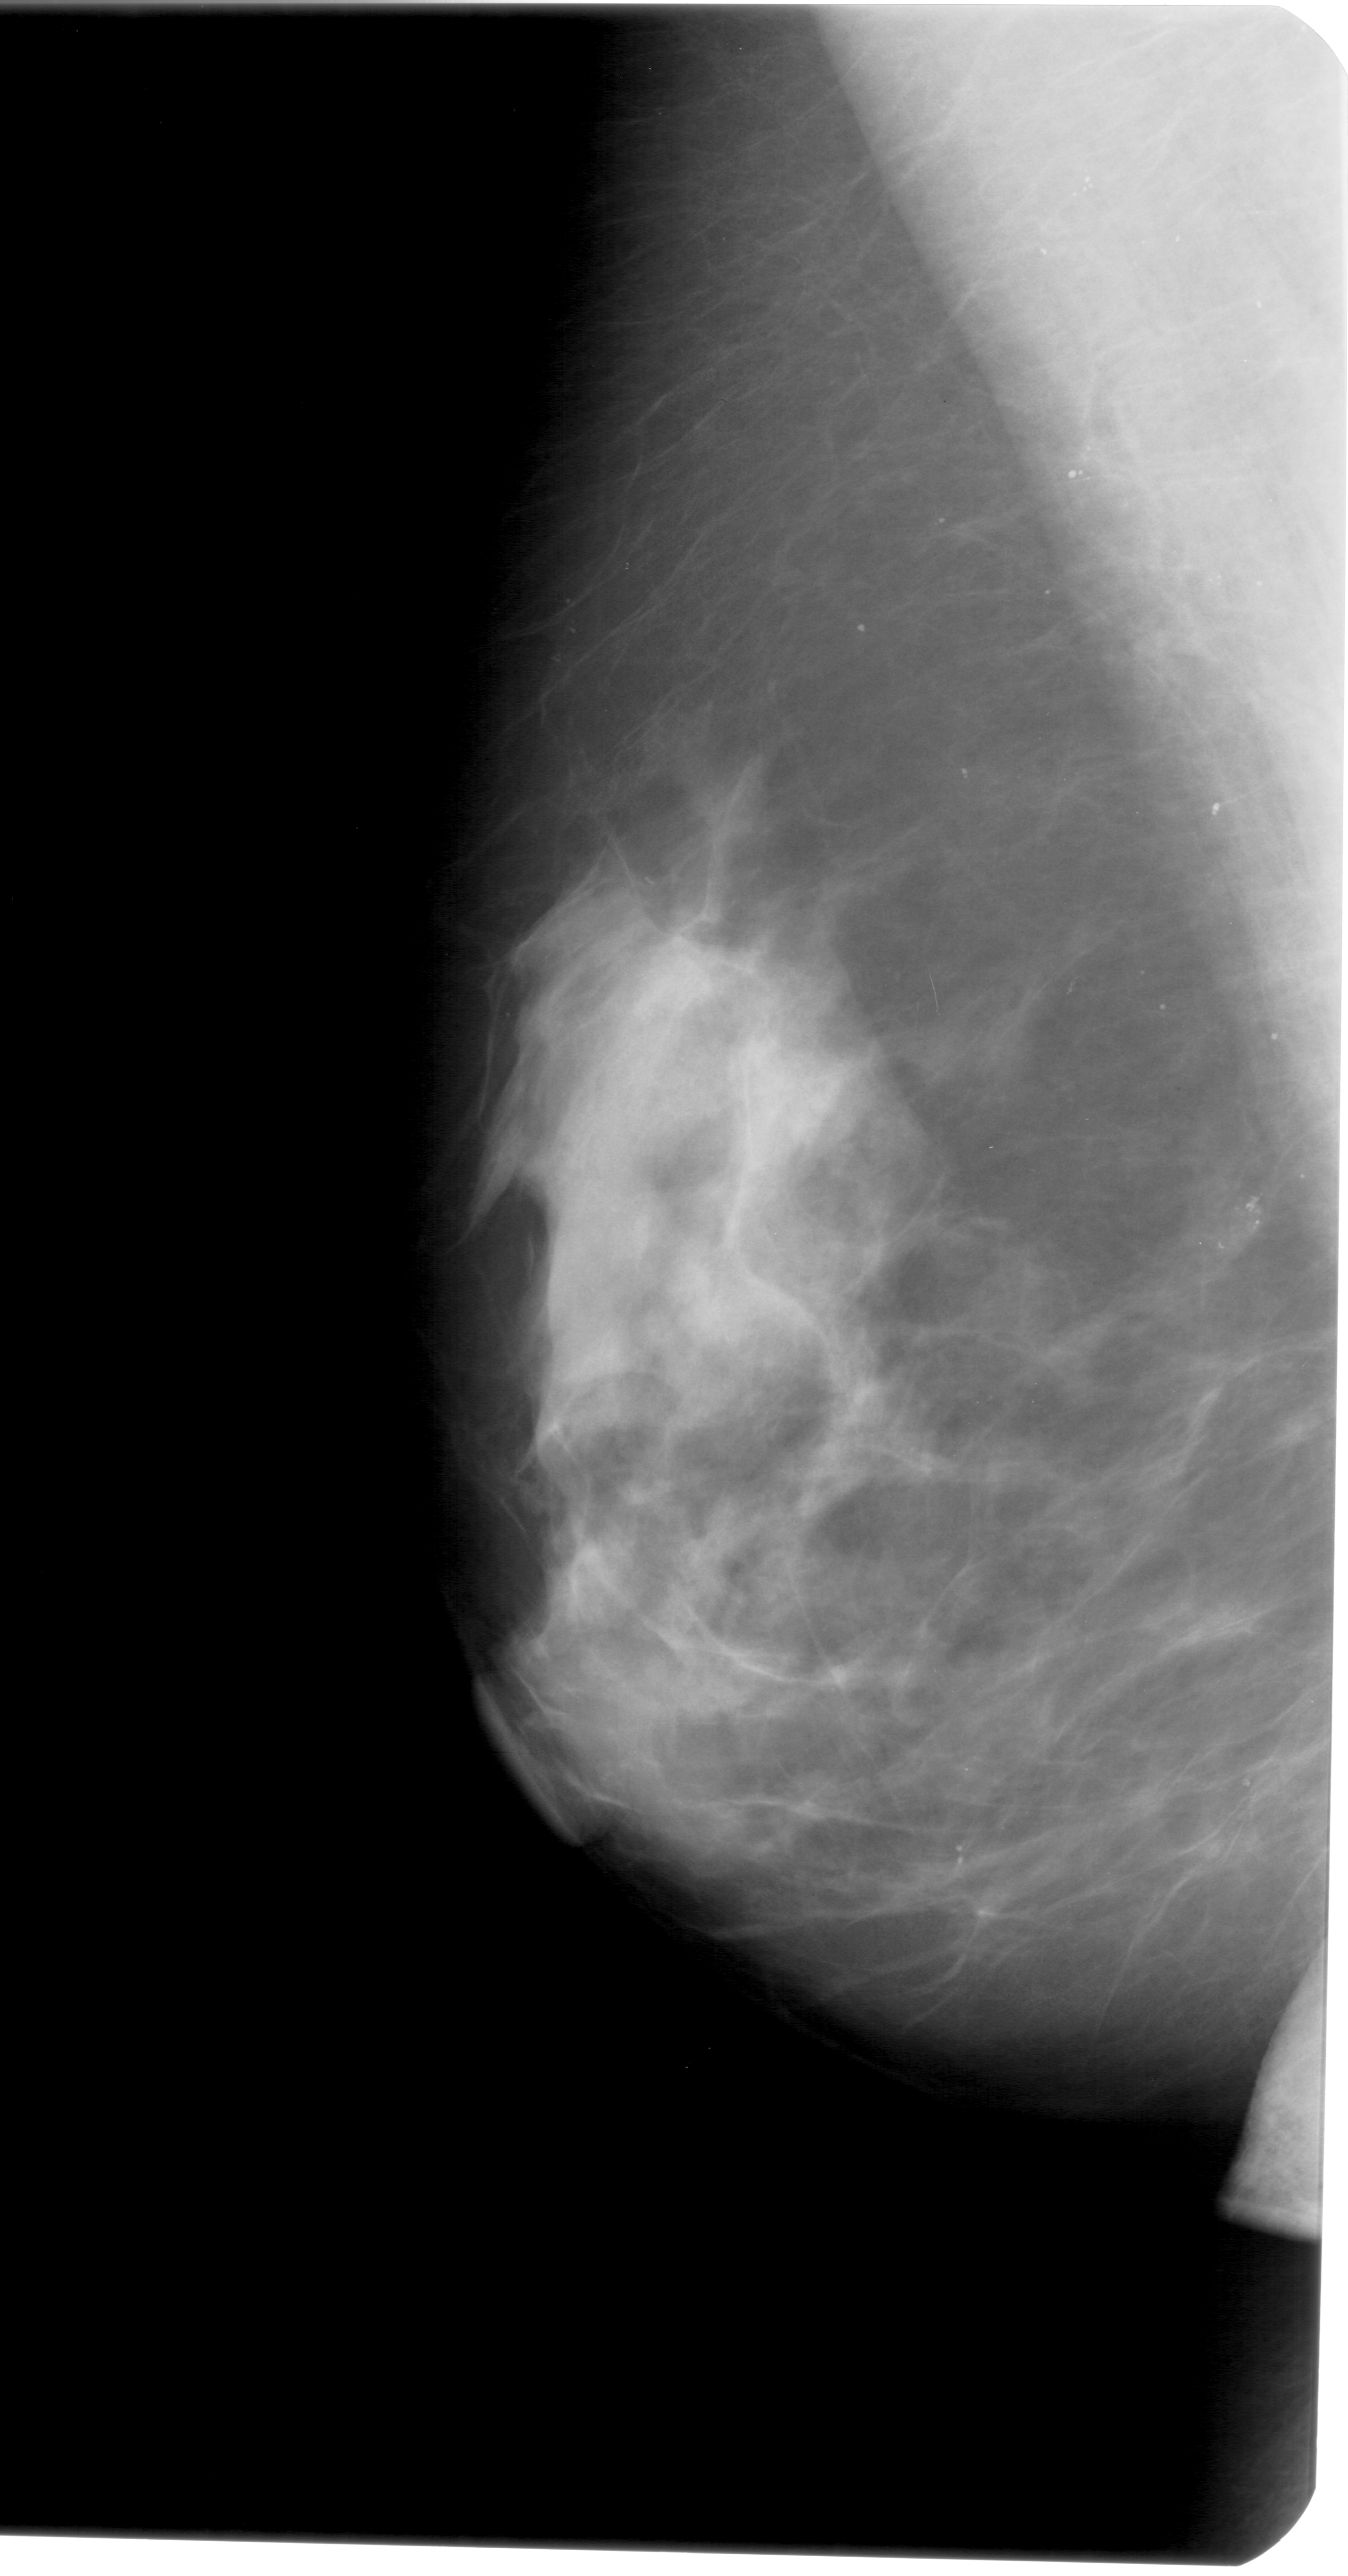
Digitized screen-film mammogram; left breast; mediolateral oblique (MLO) view.
- Finding: calcifications, morphology pleomorphic, distribution clustered; BI-RADS assessment category 4; subtlety rating 4 on a 1 (subtle) to 5 (obvious) scale; pathology (as recorded): benign.